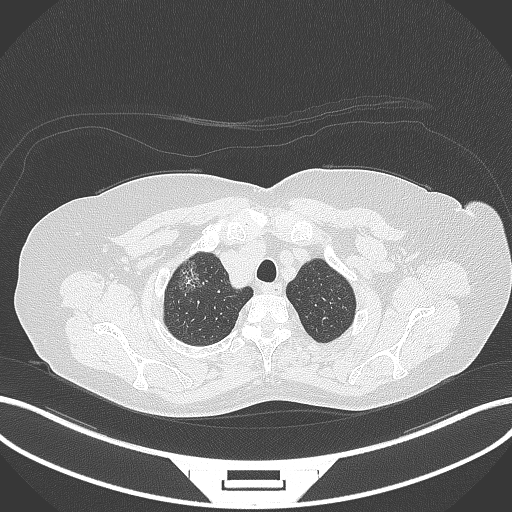
Chest CT, one axial slice. Slice 309 of 365 in the series (ordered by position). Reconstruction kernel B70f. Lung window (W 1500 / L -600 HU). 512 × 512 image matrix, field of view 400 × 400 mm. Patient: female, 62 years. From the clinical record (not read from this slice): clinical TNM (as recorded): T1c N0 M0.
Outlined on this slice (bounding box drawn by a radiologist):
- lung tumour (recorded histology: adenocarcinoma): bounding box [x1, y1, x2, y2] px = [174, 253, 208, 296]